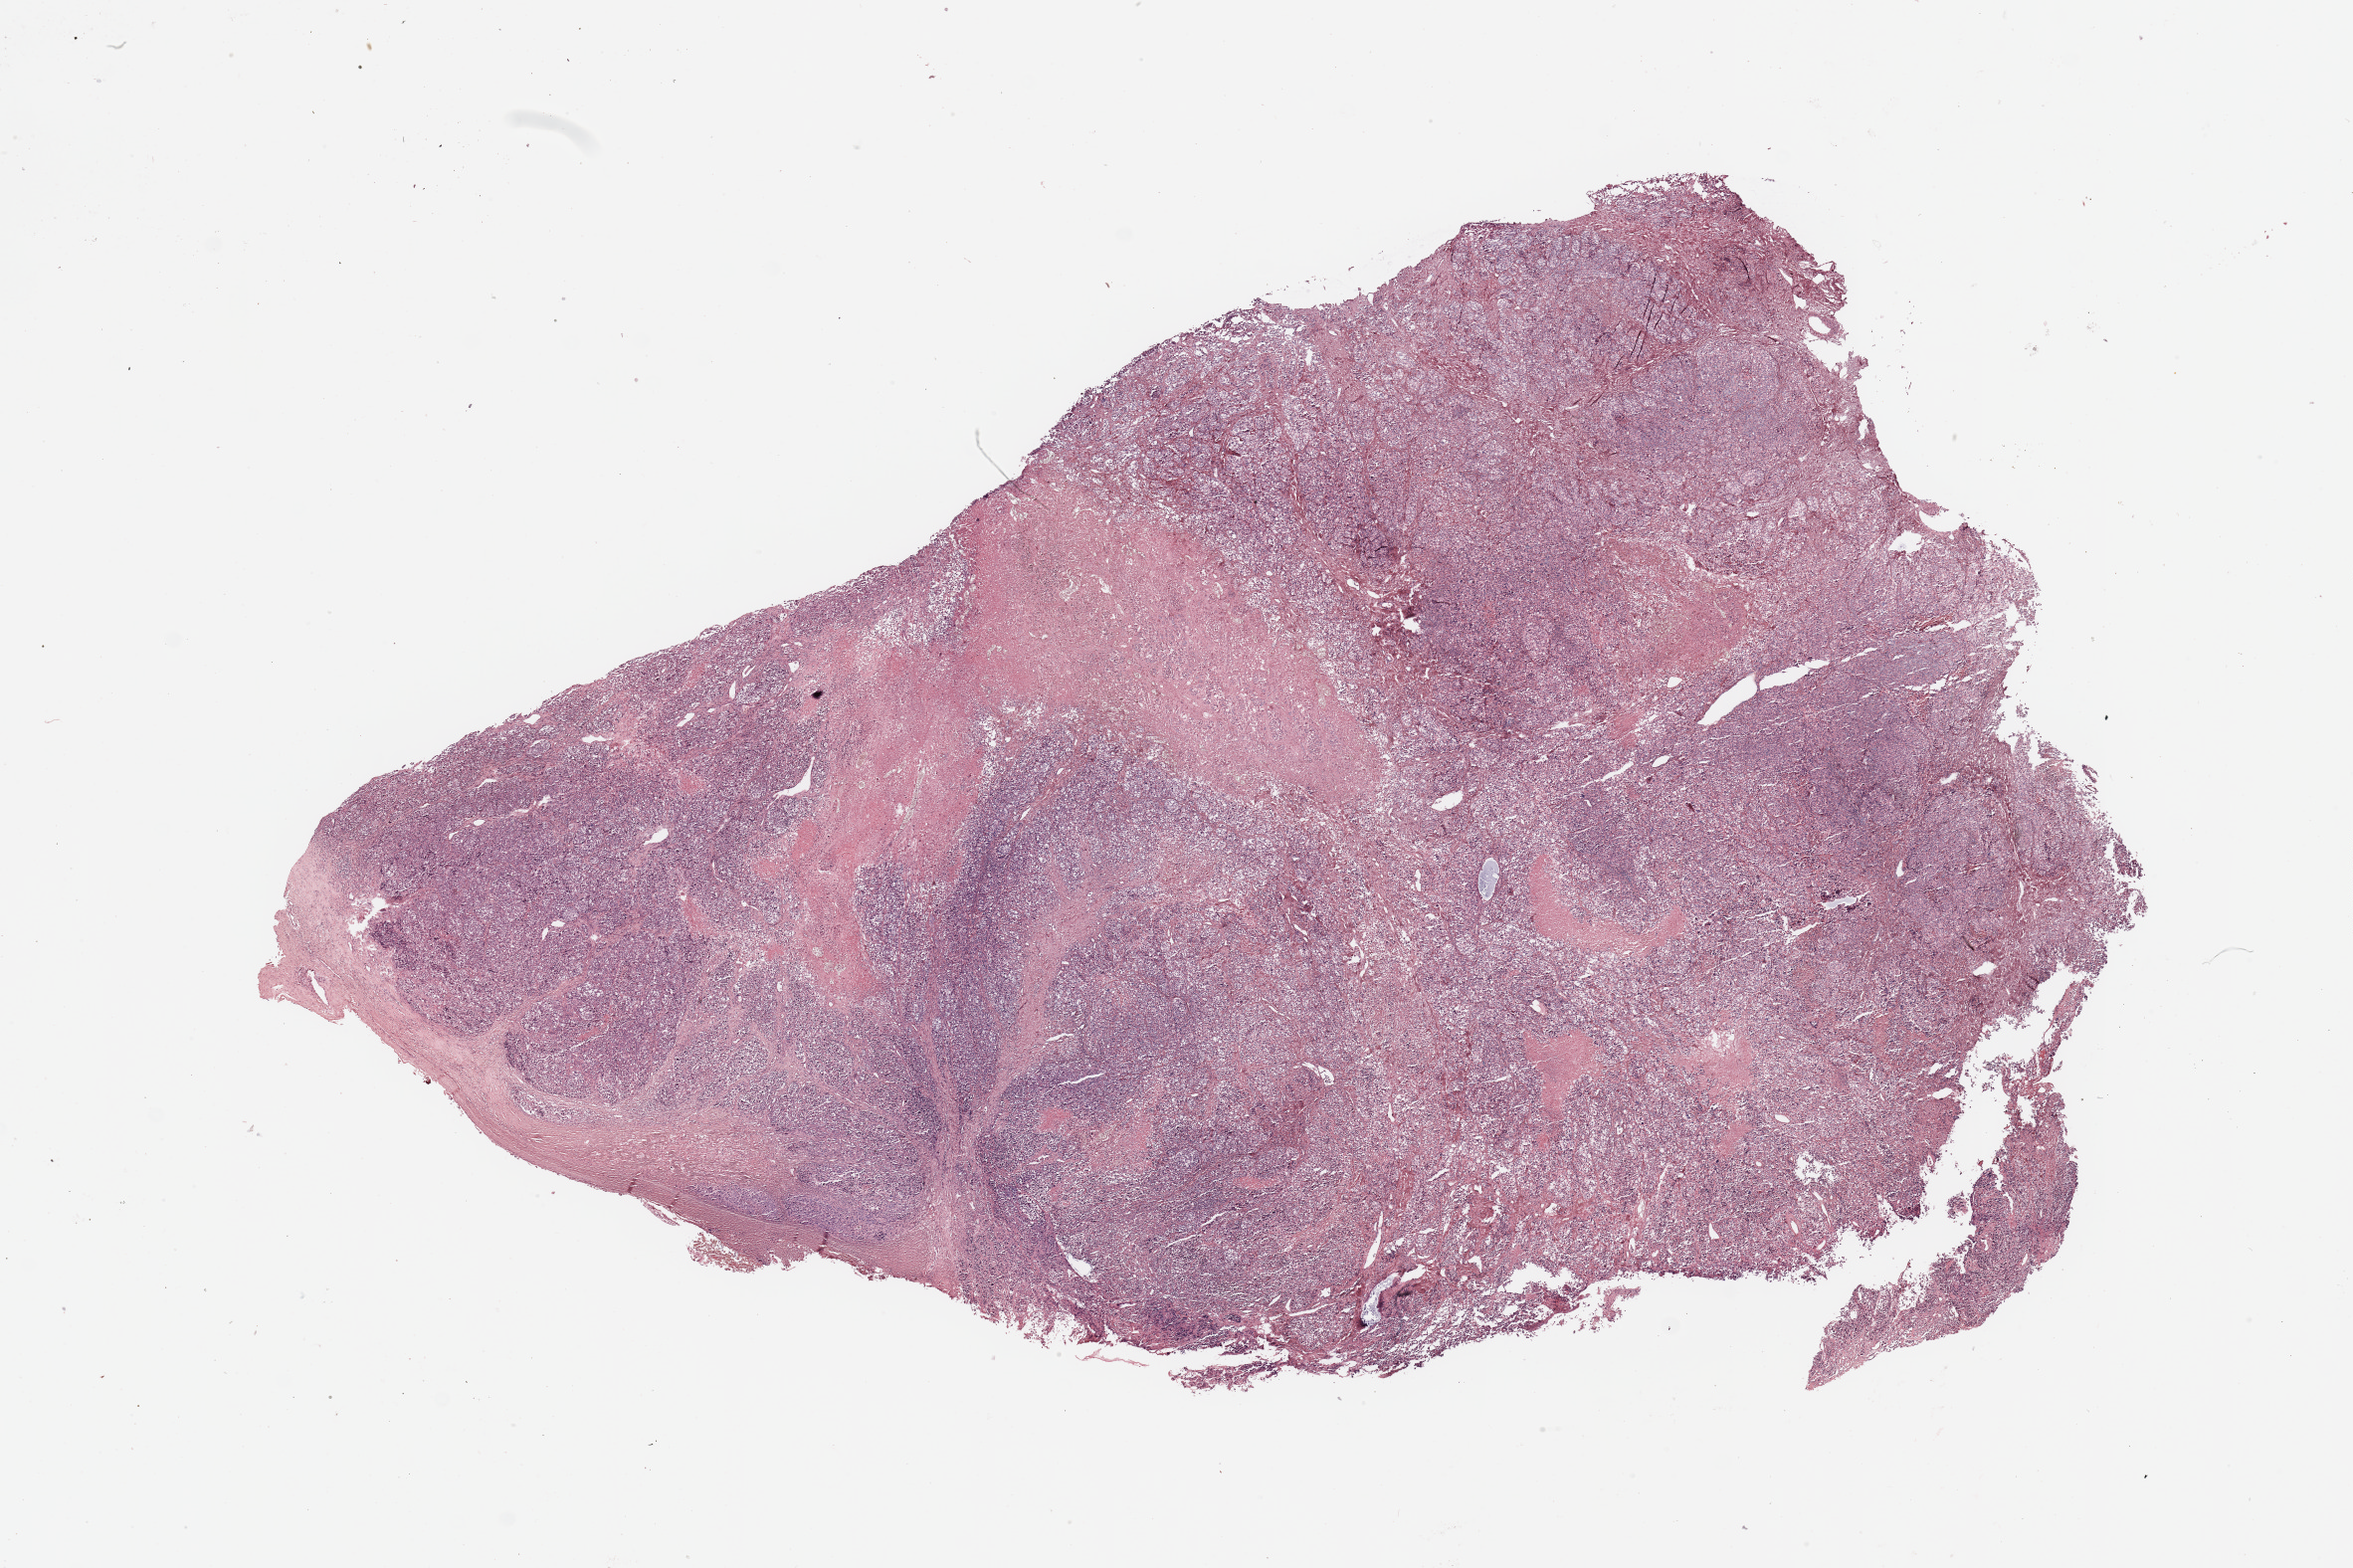
Whole-slide histology image, H&E, whole scanned area (about 18.7 x 12.5 mm) shown as a low-resolution overview. Melanoma tumour tissue; sampled site not recorded. Male, 76 y/o.
Primary tumour site (as recorded): trunk. Histologic diagnosis: Malignant melanoma, NOS. AJCC pathologic stage: IIA.